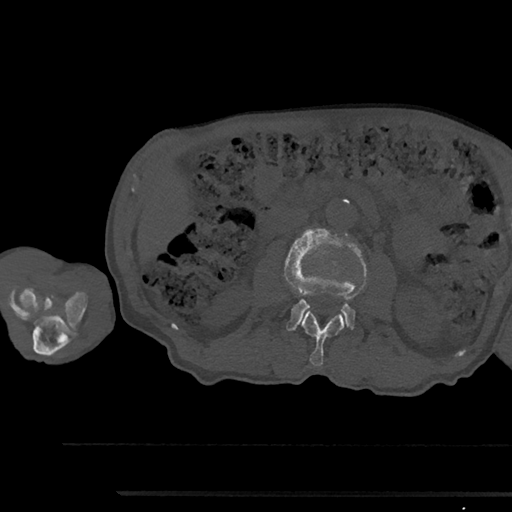
CT including the spine, one axial slice. Reconstruction kernel Br40s/3. 120 kVp. Bone window (W 1800 / L 400 HU). 512 × 512 image matrix, field of view 367 × 367 mm. Patient: male, 79 years. From the clinical record (not read from this slice): primary cancer: prostate.
Structures marked on this image (semi-automatically segmented with operator editing):
- L2 vertebra: bounding box <301,310,345,366> (left, top, right, bottom; pixels)
- L3 vertebra: <284,229,368,331>